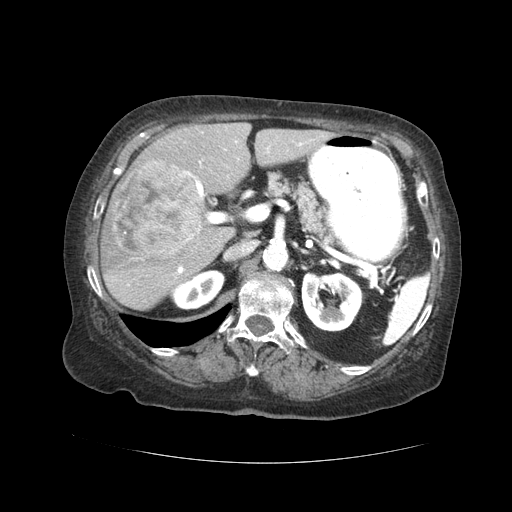
Contrast-enhanced abdominal CT (liver protocol), one axial slice; reconstruction kernel STANDARD; 120 kVp; soft-tissue window (W 400 / L 40 HU); 2.5 mm slice thickness; 512 × 512 image matrix. Case-level facts recorded for this patient, not image findings: diagnosis: hepatocellular carcinoma (patient treated with transarterial chemoembolisation; whether this scan precedes or follows treatment is not stated here); TNM stage (as recorded): Stage-I; Child-Pugh class: A.
Structures marked on this image (semi-automatic segmentation, software-assisted and operator-edited):
- liver parenchyma outside the tumour (the mass and vessels are separate outlines, so this box may not span the whole liver): bounding box (x1, y1, x2, y2) in pixels: (100, 122, 331, 310)
- mass: (109, 160, 203, 257)
- liver vessels: (177, 140, 312, 274)